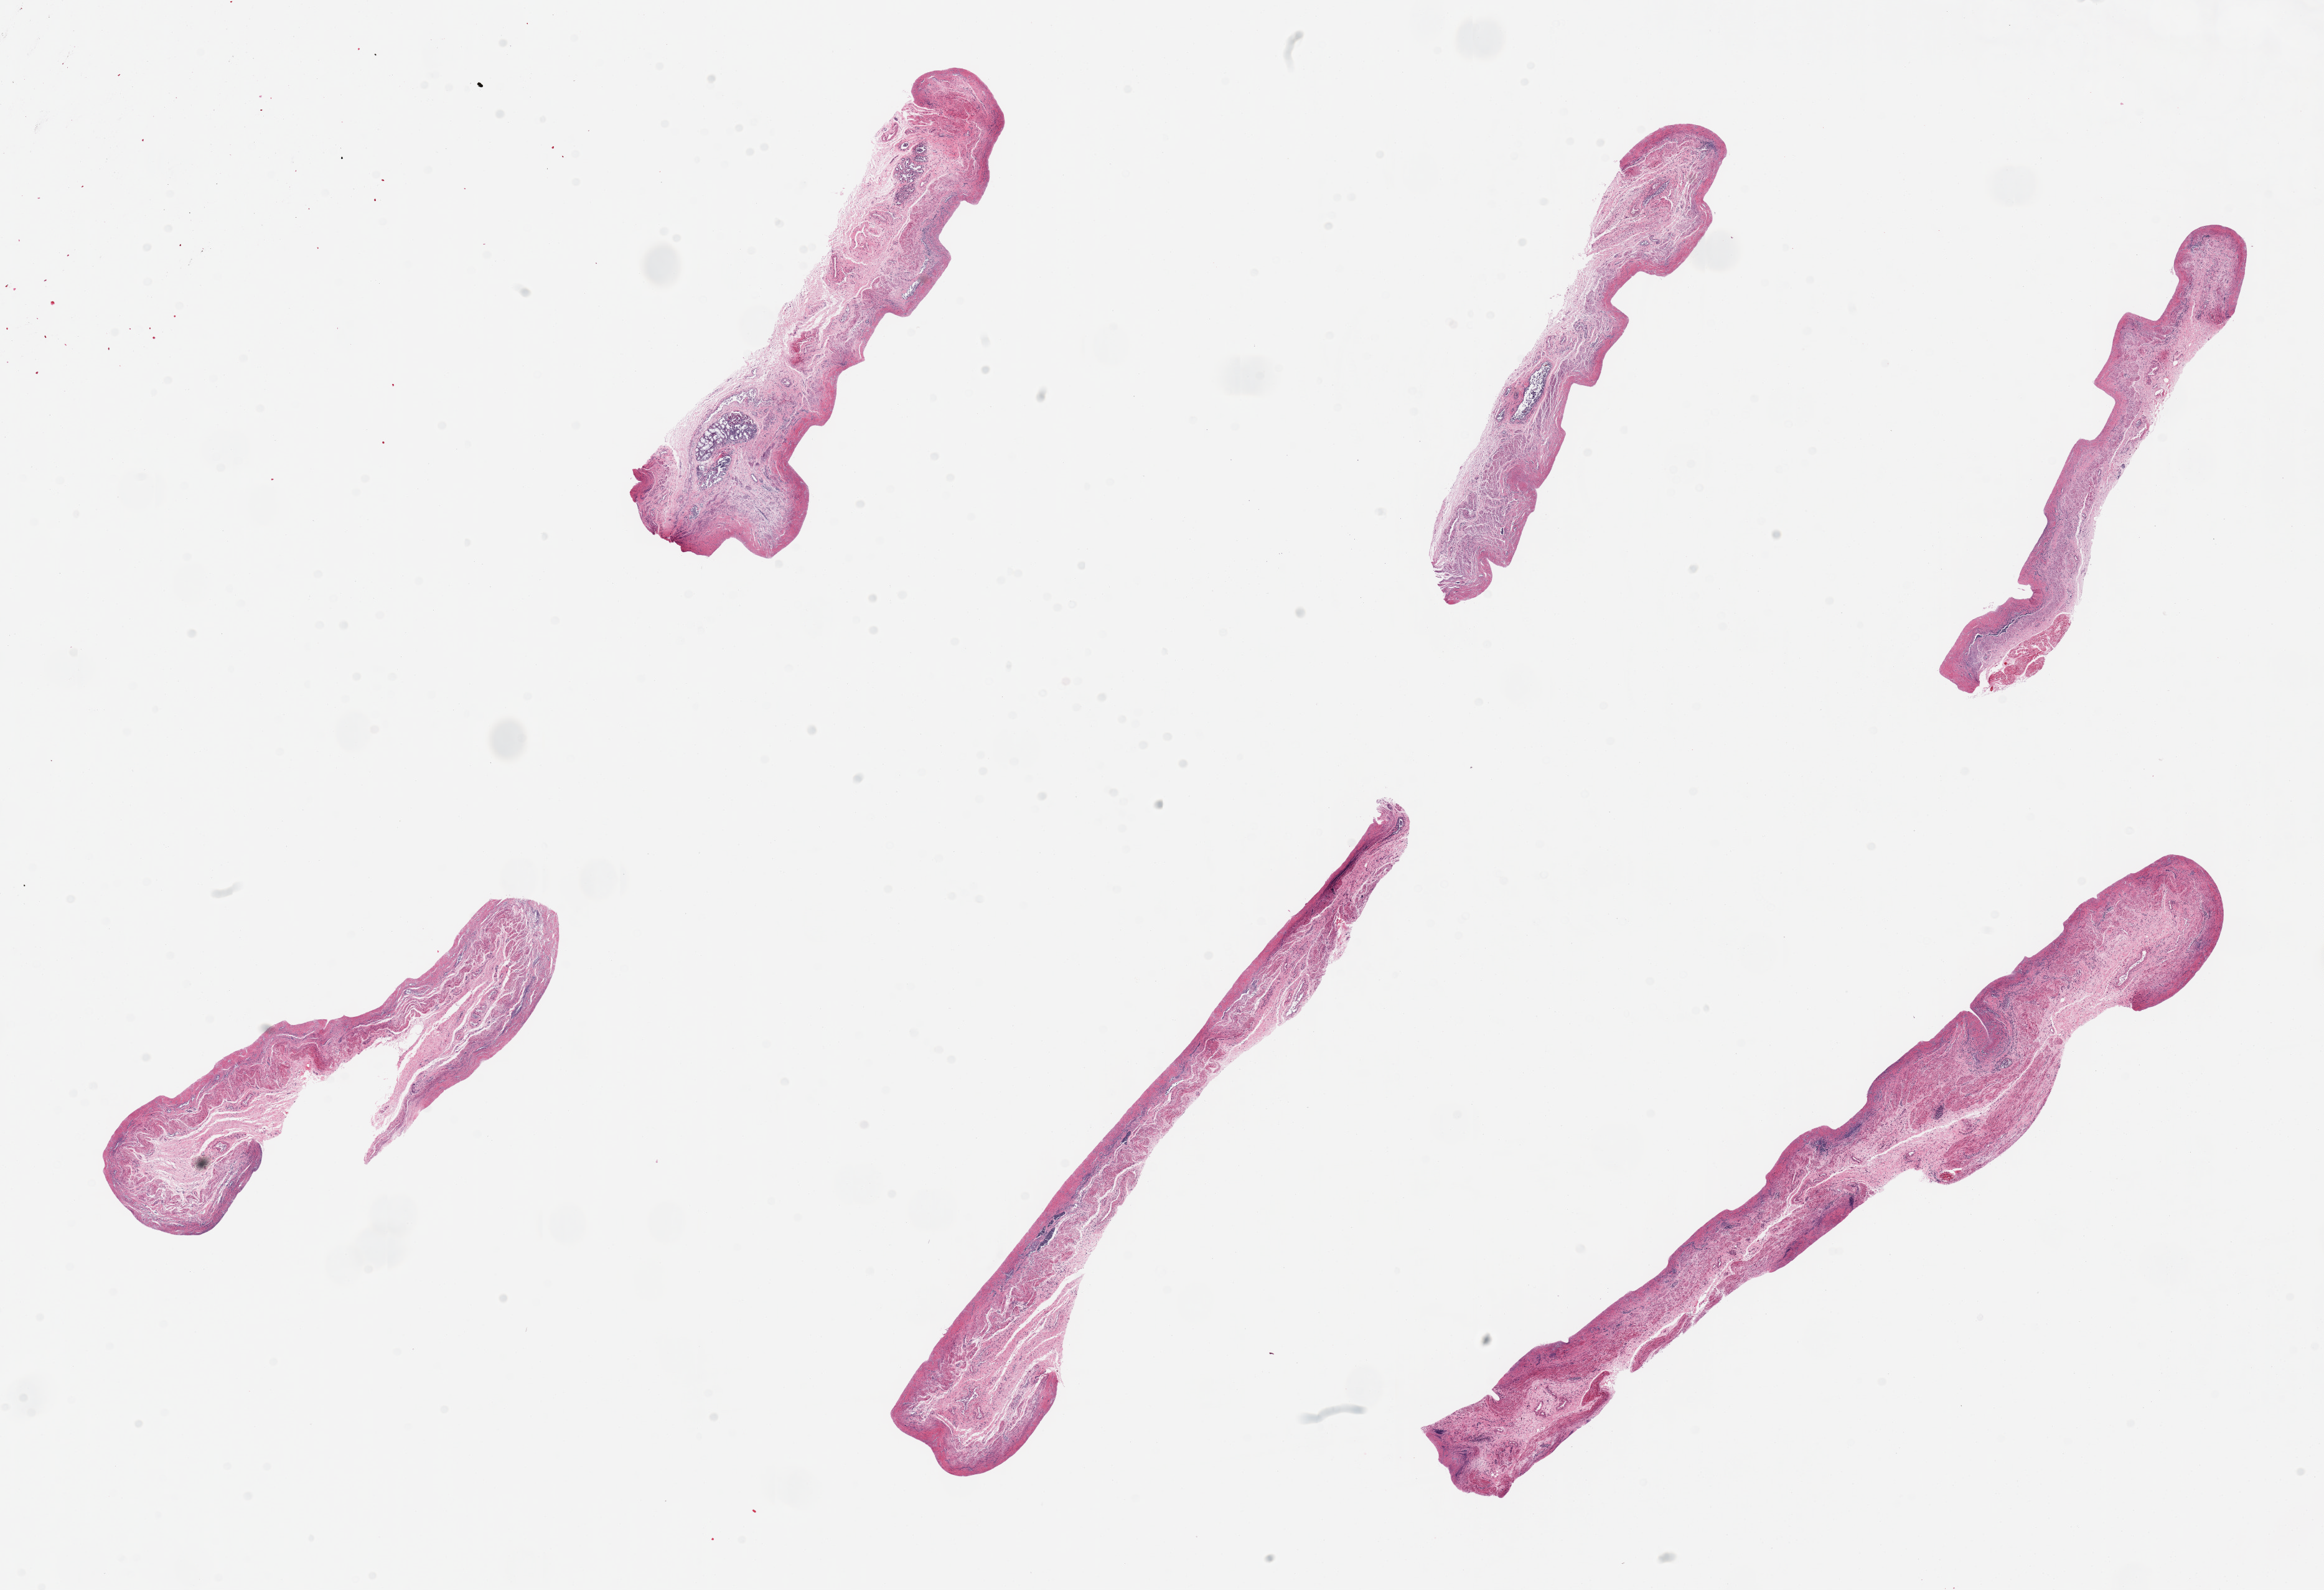
Digitized H&E-stained section — shown as a low-resolution overview of the whole scanned area (about 29.5 x 20.2 mm, from a 20x scan); PAXgene-fixed, paraffin-embedded tissue; section of esophageal mucous membrane (target tissue); donor tissue sample. Donor: female.
- reviewer comment on this tissue sample: 6 pieces, near- total autolysis/mucosa completely sloughed